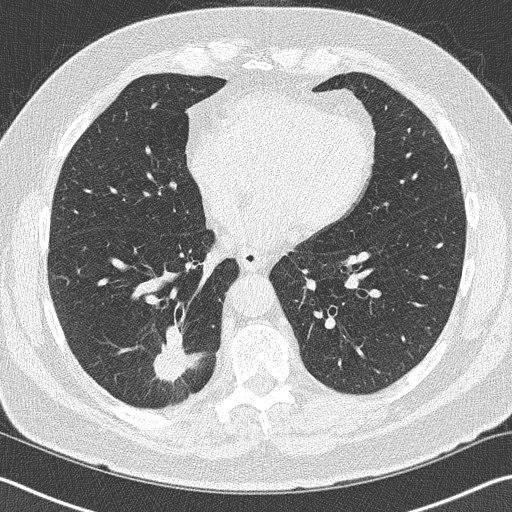
Chest CT (low-dose screening protocol), one axial image, baseline annual screen, lung window (W 1500 / L -600 HU), 2 mm slice thickness, lung (sharp) reconstruction kernel (B50f), 120 kVp. Male participant, aged 70 years at enrolment. Current smoker at enrolment.
- Expert-annotated lung lesion, bounding box [x1, y1, x2, y2] px = [140, 328, 212, 400].
- The exam's reader record, not a measurement of the box and not confirmed to be the same lesion: non-calcified nodule or mass ≥4 mm, right lower lobe, 28 × 23 mm, spiculated (stellate) margins, soft tissue attenuation.
- Official screen result: positive, change unspecified: nodule(s) >= 4 mm or enlarging nodule(s), mass(es), or other non-specific abnormalities suspicious for lung cancer.
- Later outcome: lung cancer diagnosed 62 days after this screen — squamous cell carcinoma, NOS, right lower lobe, poorly differentiated (G3), stage IB (AJCC 6th edition), 24 mm at pathology.